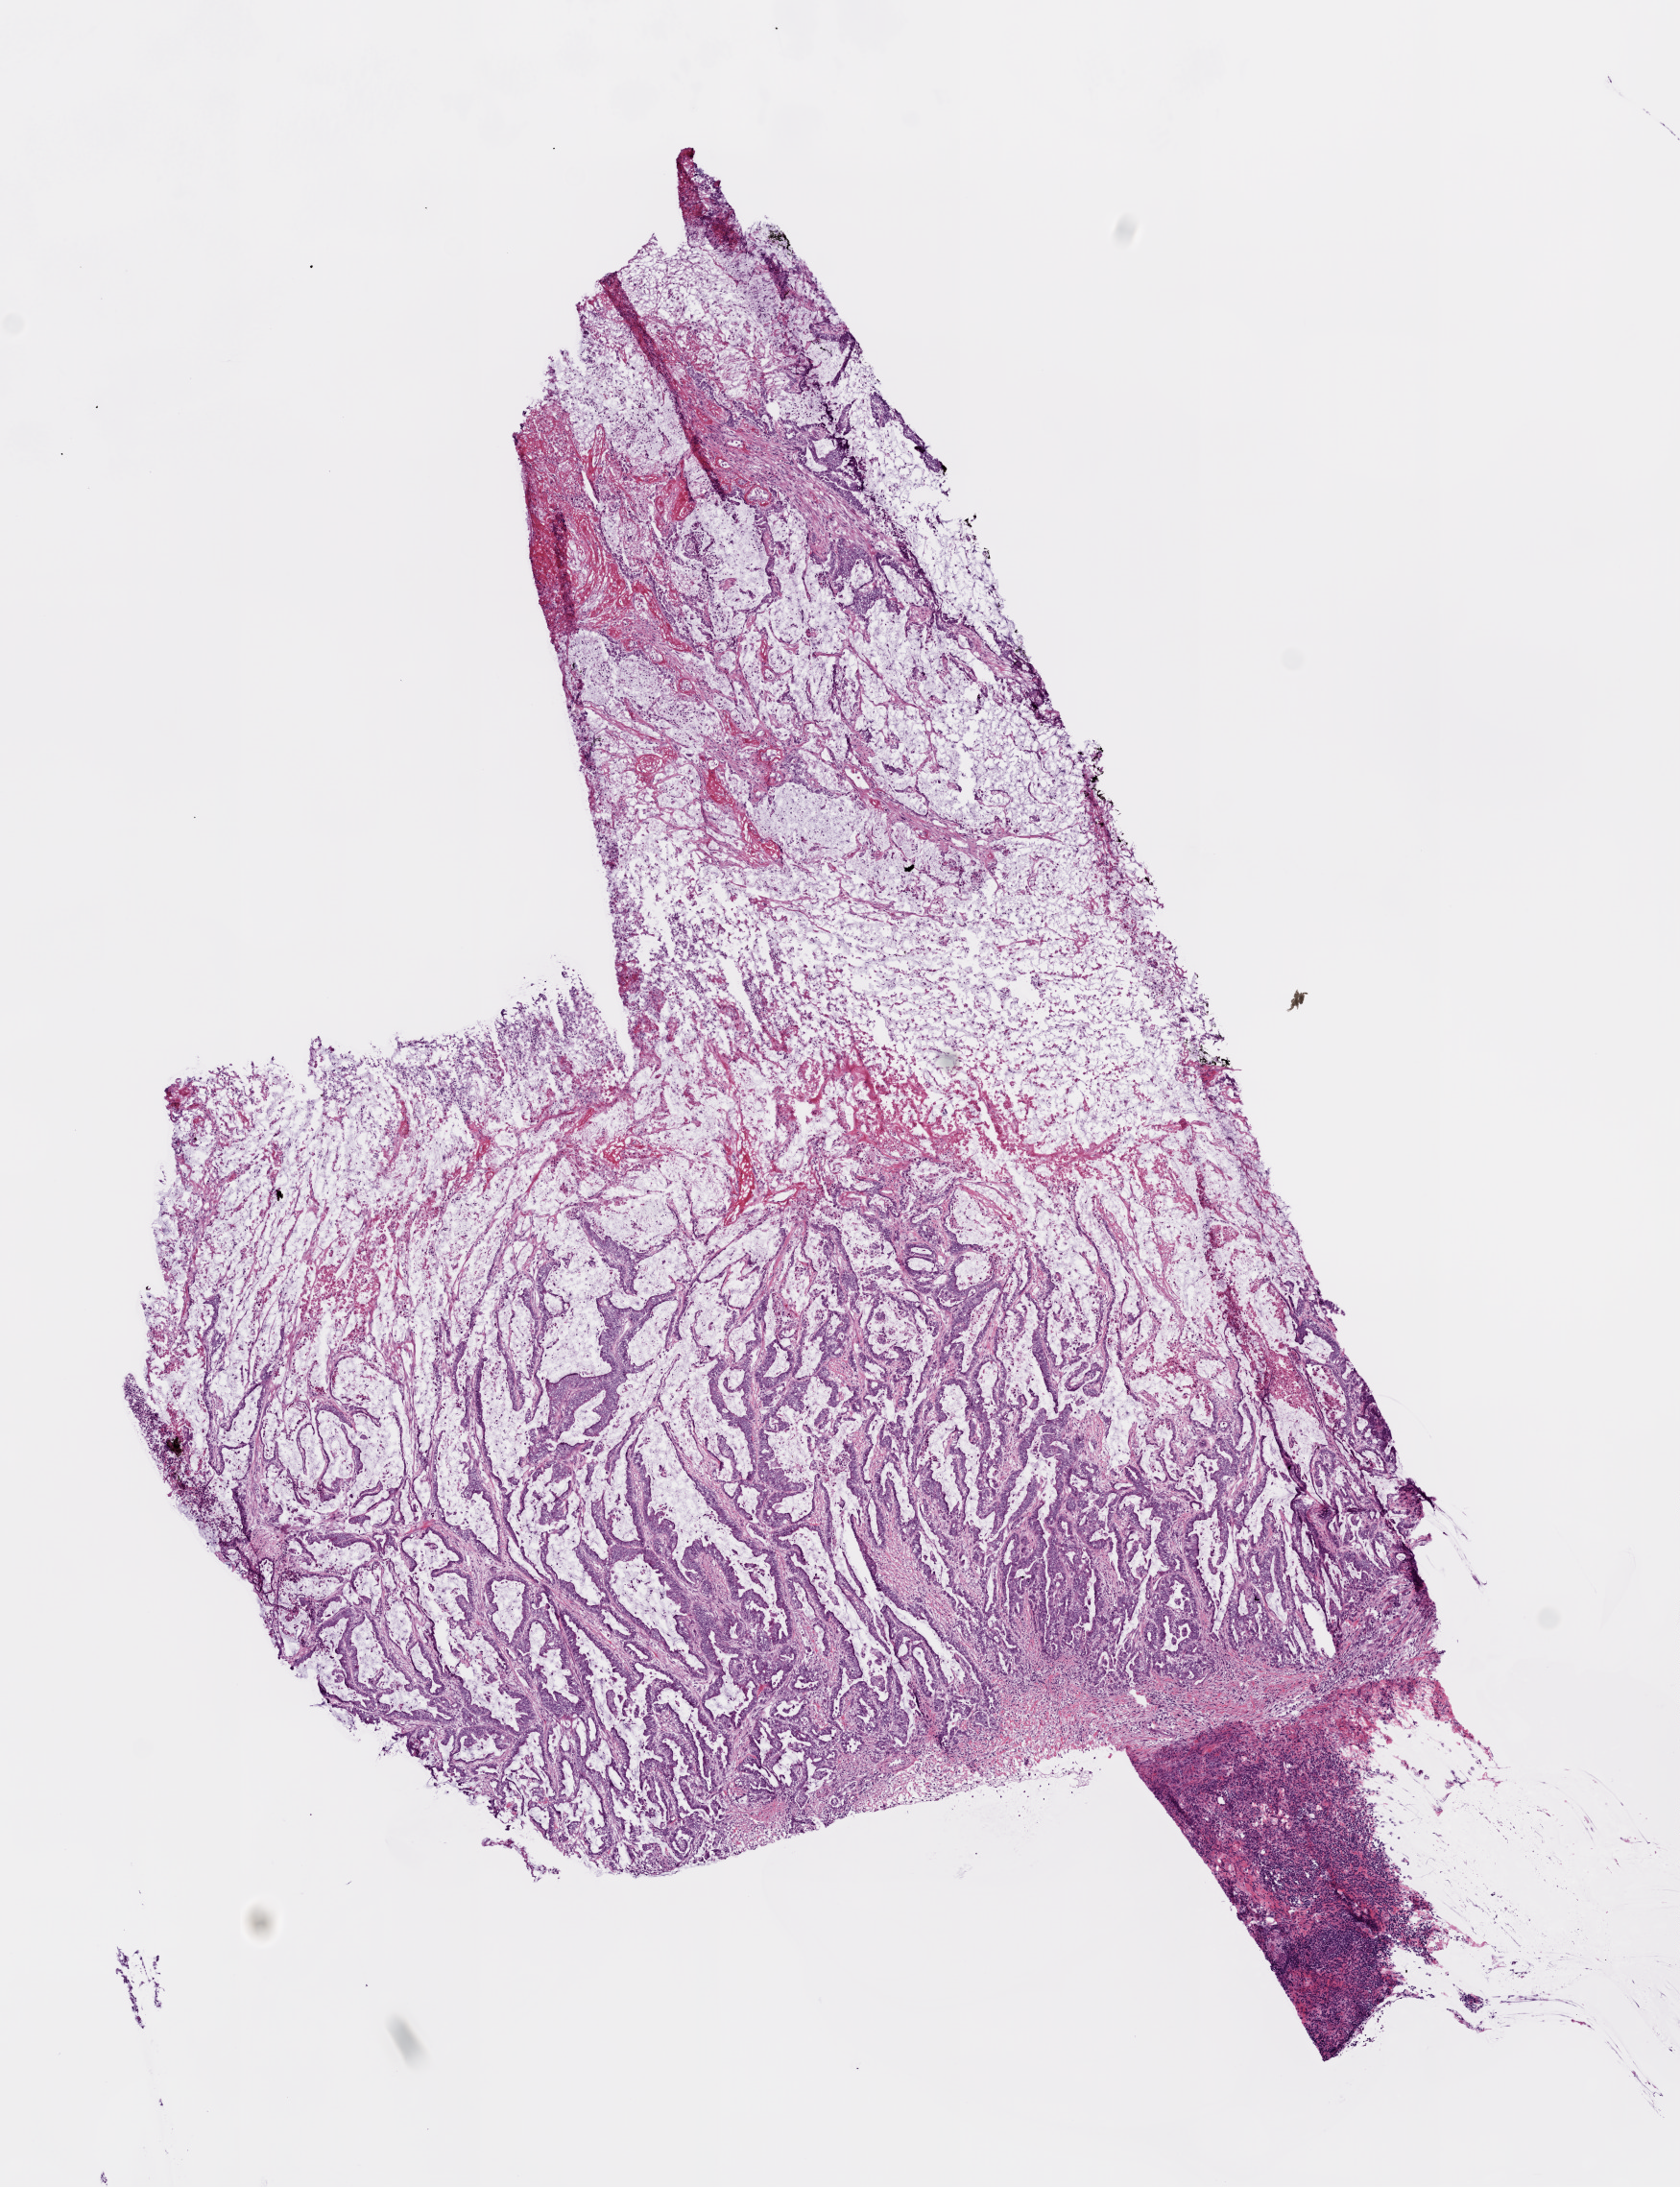
Whole-slide histology image, Hematoxylin and eosin (H&E) stained, a low-resolution overview of the entire scanned area, about 7.0 x 9.1 mm. Frozen section from the bottom of the tissue portion. Sample: primary tumour, colon. Female, age 84 years at initial diagnosis. Pathologist review of this section (percent, as recorded): tumour cells 60%, tumour nuclei 70%, normal cells 0%, stromal cells 20%, necrosis 20%. Inflammatory infiltration, as recorded: lymphocyte infiltration 15%, monocyte infiltration 0%, neutrophil infiltration 0%.
AJCC pathologic stage: IIA (7th edition). Pathologic diagnosis: Adenocarcinoma, NOS (ascending colon). TNM: T3 N0 M0.